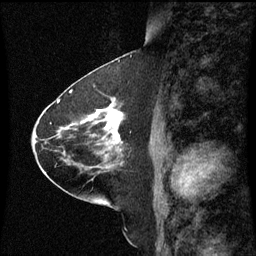
Breast MRI (dynamic contrast-enhanced), one sagittal slice; position 32 of 60 along the scan axis; dynamic contrast-enhanced series, image 2 of 3 at this slice position (ordered by acquisition); 1.5 T; TE 4.2 ms, TR 8.9 ms; 2 mm slice thickness; 256 × 256 image matrix, field of view 200 × 200 mm. Female patient, age 63 years. From the clinical record (not read from this slice): setting: breast cancer imaged before/during neoadjuvant chemotherapy; receptor status: HR-positive, HER2-negative.
Outlined on this slice (semi-automatically segmented with operator editing):
- analysis volume of interest (the breast-tissue region the enhancement analysis was run in; not a lesion): box from (x=77, y=100) to (x=126, y=151) px
- tumour enhancement mask (voxels above the 70 % enhancement threshold inside the analysis volume of interest): (x=95, y=104)–(x=121, y=141)